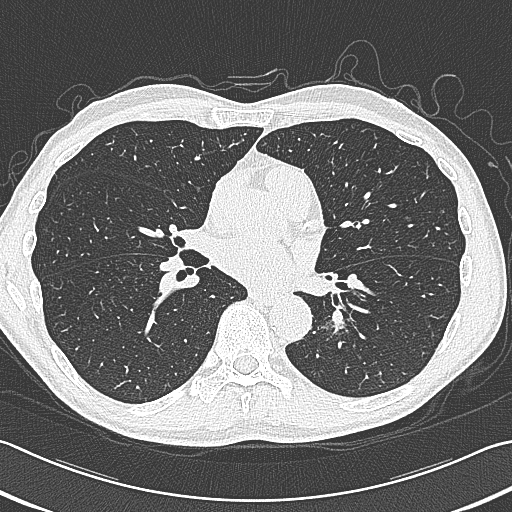
Chest CT (low-dose screening protocol), one axial image. First (baseline) screen. Lung window (W 1500 / L -600 HU). 120 kVp. 512 × 512 image matrix, field of view 346 × 346 mm. Male, age 59 years at enrolment. Former smoker at enrolment.
• Expert reader's lesion annotation, bounding box (x1, y1, x2, y2) in pixels: (311, 296, 377, 354).
• Screening reader's record for this exam (one nodule recorded; not confirmed to be the boxed lesion): non-calcified nodule or mass ≥4 mm, left lower lobe, 15 × 15 mm, smooth margins, soft tissue attenuation.
• Participant outcome: lung cancer diagnosed 17 days after this screen — squamous cell carcinoma, large cell, nonkeratinizing, NOS, left lower lobe, poorly differentiated (G3), stage IB (AJCC 6th edition), 31 mm at pathology.